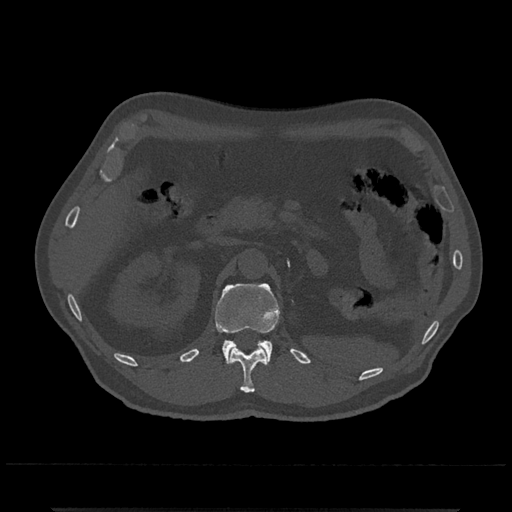
CT including the spine, one axial slice; slice 393 of 797 in the series (ordered by position); reconstruction kernel Br40s/3; 120 kVp; bone window (W 1800 / L 400 HU); 0.5 mm slice thickness; 512 × 512 image matrix. Patient: male, 67 years. Case-level facts recorded for this patient, not image findings: primary cancer: prostate.
Outlined on this slice (semi-automatically segmented with operator editing):
- L1 vertebra: bounding box <215,283,280,364> (left, top, right, bottom; pixels)
- T12 vertebra: <230,346,268,393>